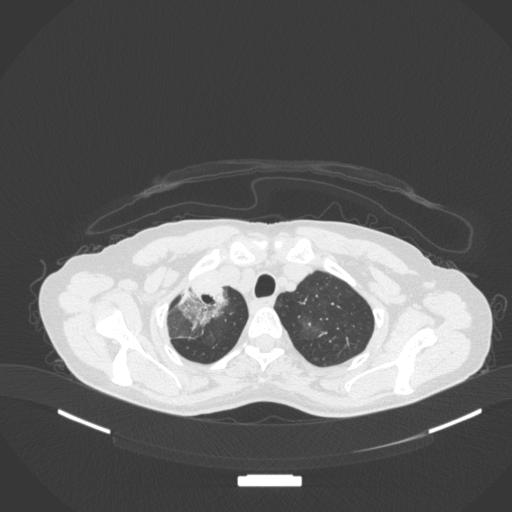
Chest CT, one axial slice. Slice 281 of 311 in the series (ordered by position). 120 kVp. Lung window (W 1500 / L -600 HU). 512 × 512 image matrix, field of view 400 × 400 mm. Female patient, age 59 years. From the clinical record (not read from this slice): clinical TNM (as recorded): T3 N0 M0; histopathological grade: G1.
Annotated regions visible in this slice (bounding box drawn by a radiologist):
- lung tumour (recorded histology: adenocarcinoma): bounding box (x1, y1, x2, y2) in pixels: (169, 279, 227, 328)